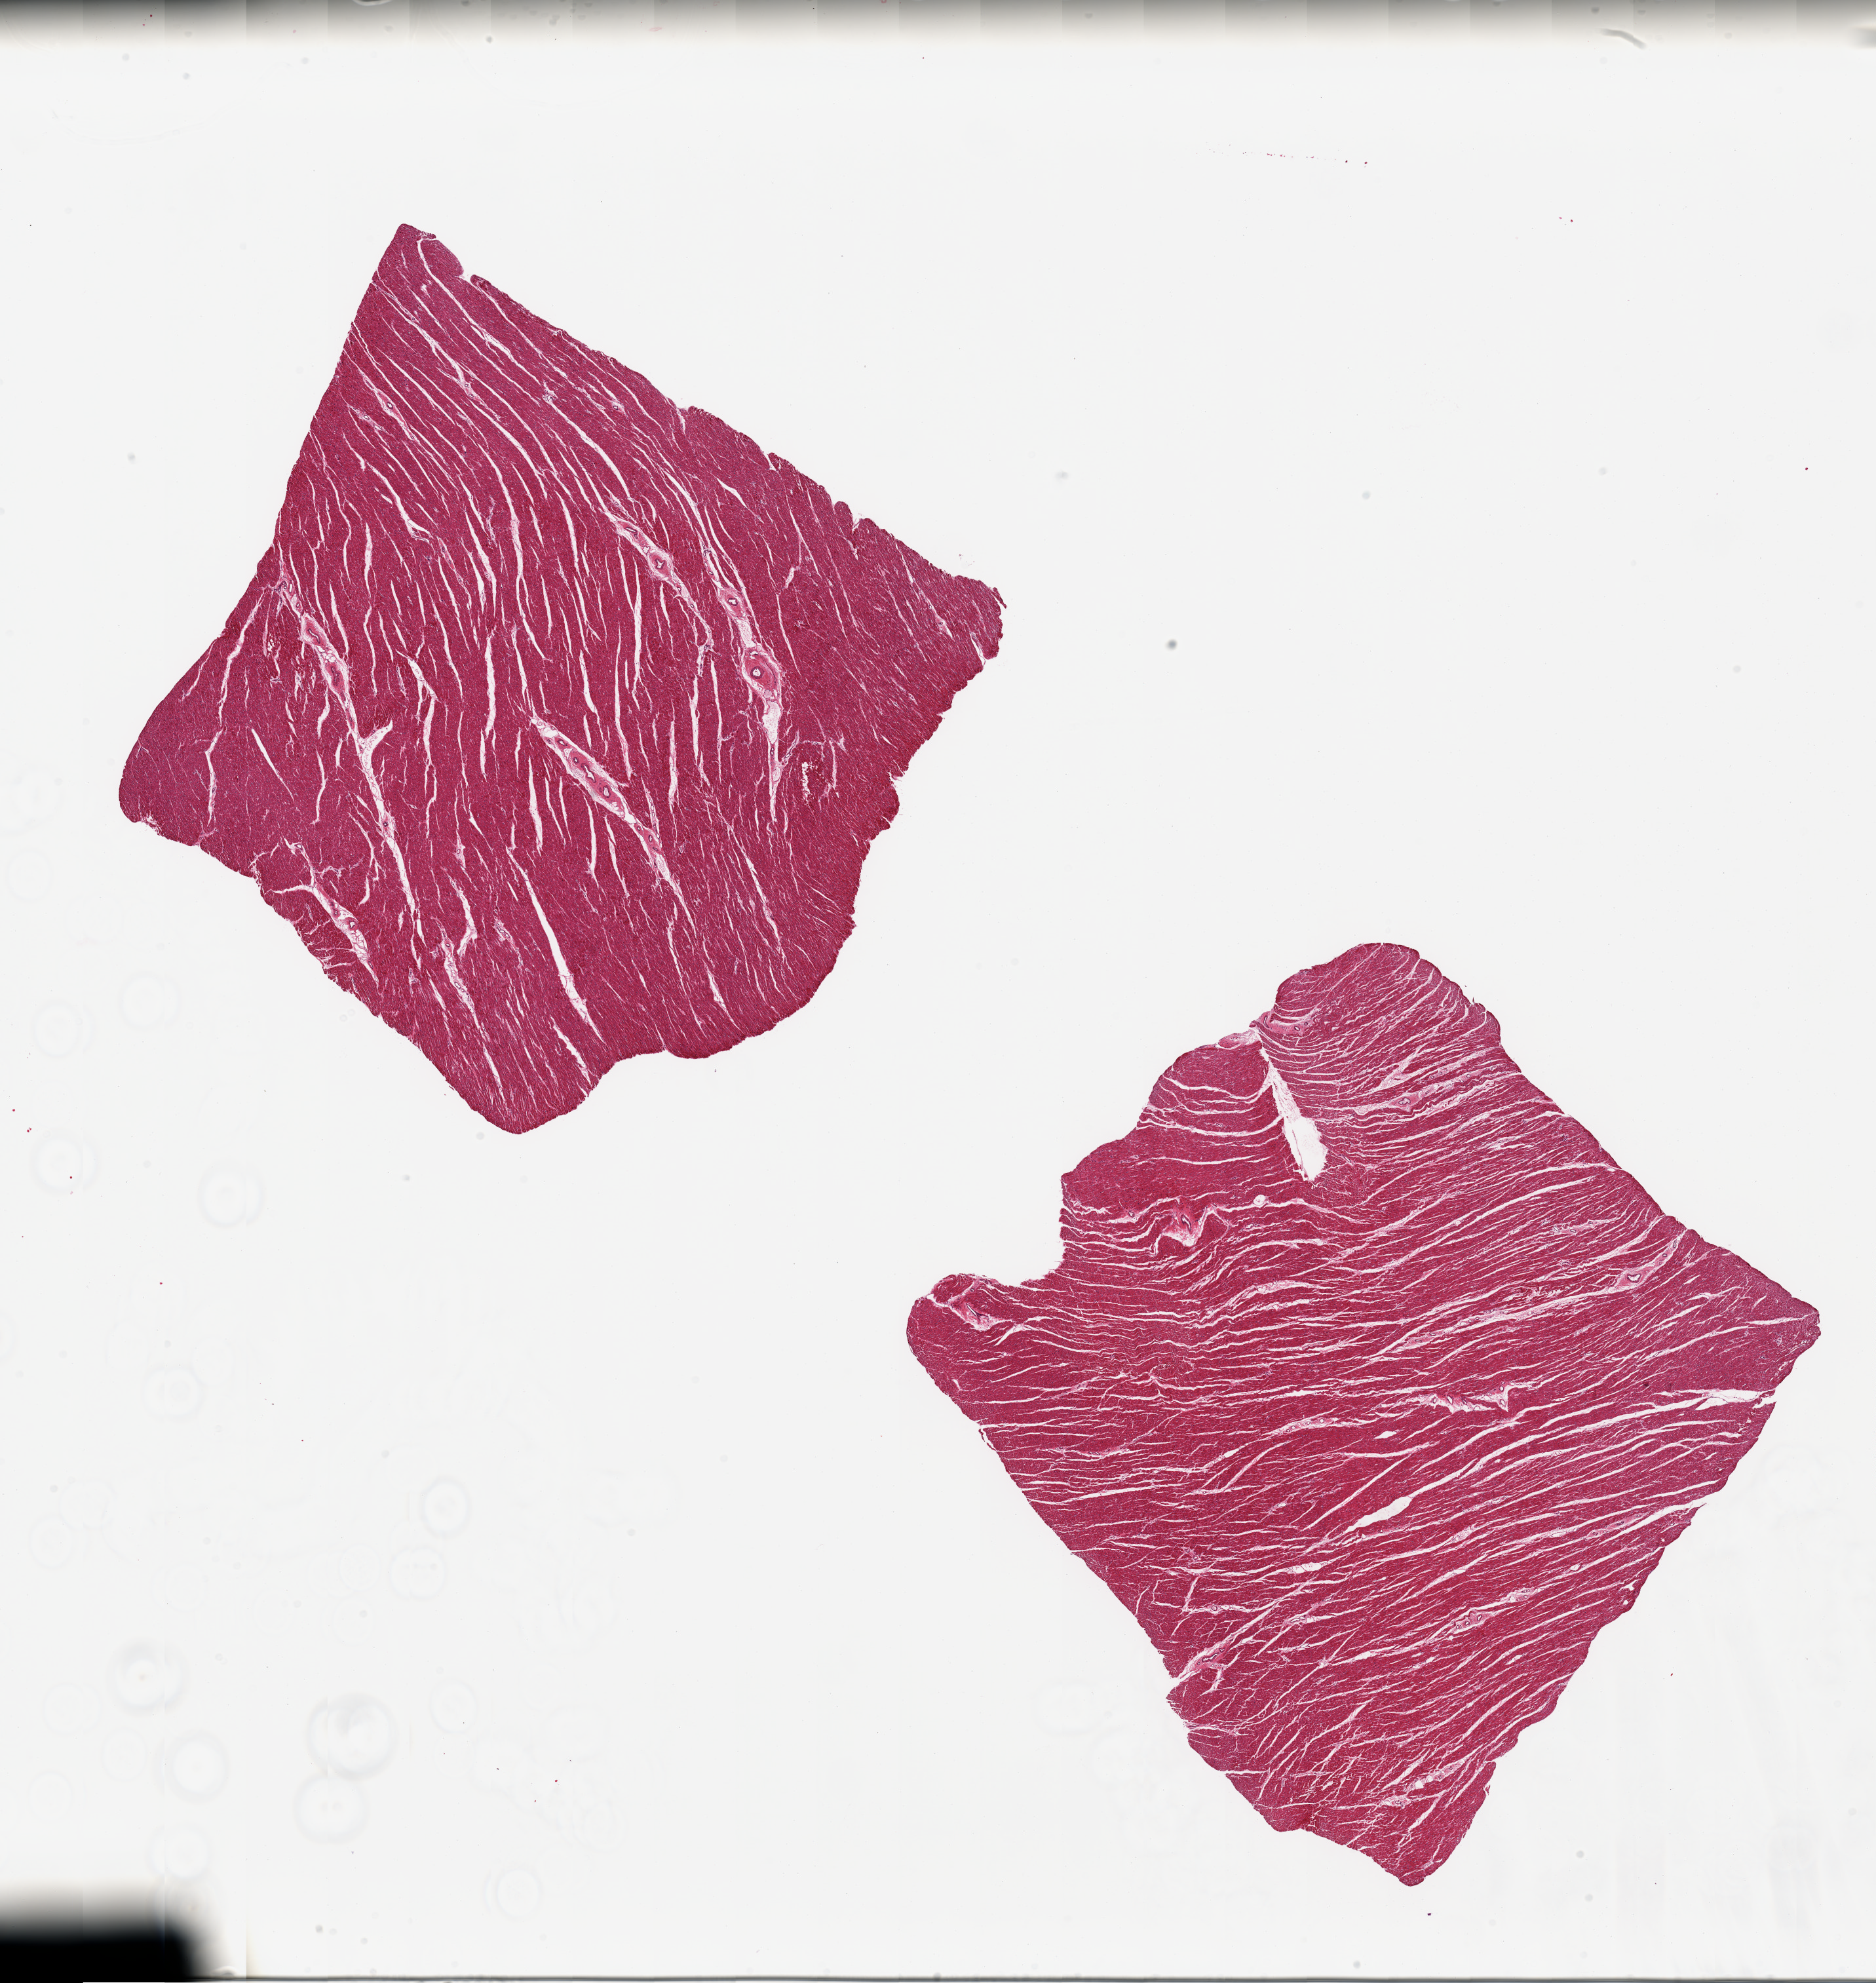
Whole-slide image, hematoxylin and eosin (H&E) stain — low-resolution overview of the scanned area, about 22.6 x 23.9 mm (acquisition: 20x scan), PAXgene-fixed paraffin-embedded (PFPE) section, target tissue: heart, donor tissue sample.
* review note (as recorded): 2 pieces